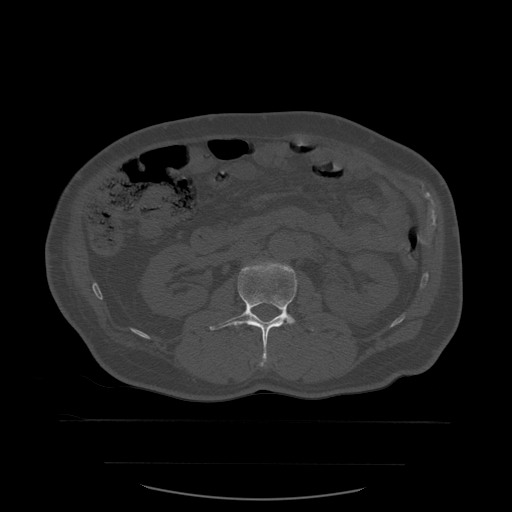
CT including the spine, one axial slice. Slice 218 of 590 in the series (ordered by position). Bone window (W 1800 / L 400 HU). 1.25 mm slice thickness. 512 × 512 image matrix. Patient age 71 years. Case-level facts recorded for this patient, not image findings: primary cancer: lung.
Outlined on this slice (semi-automatic segmentation, software-assisted and operator-edited):
- L2 vertebra: bounding box (x1, y1, x2, y2) in pixels: (210, 261, 320, 367)